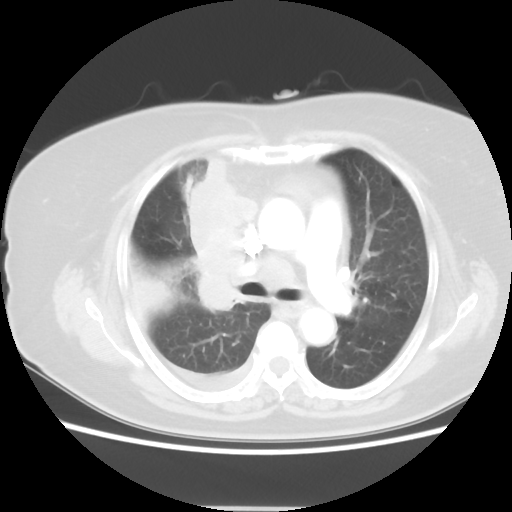
Chest CT, one axial slice. Slice 30 of 48 in the series (ordered by position). Reconstruction kernel STANDARD. Lung window (W 1500 / L -600 HU). 5 mm slice thickness. 512 × 512 image matrix, field of view 360 × 360 mm. Patient: female, 73 years. Case-level facts recorded for this patient, not image findings: clinical TNM (as recorded): T3 N3 M1b.
Structures marked on this image (bounding box drawn by a radiologist):
- lung tumour (recorded histology: small cell carcinoma): box from (x=169, y=150) to (x=265, y=311) px